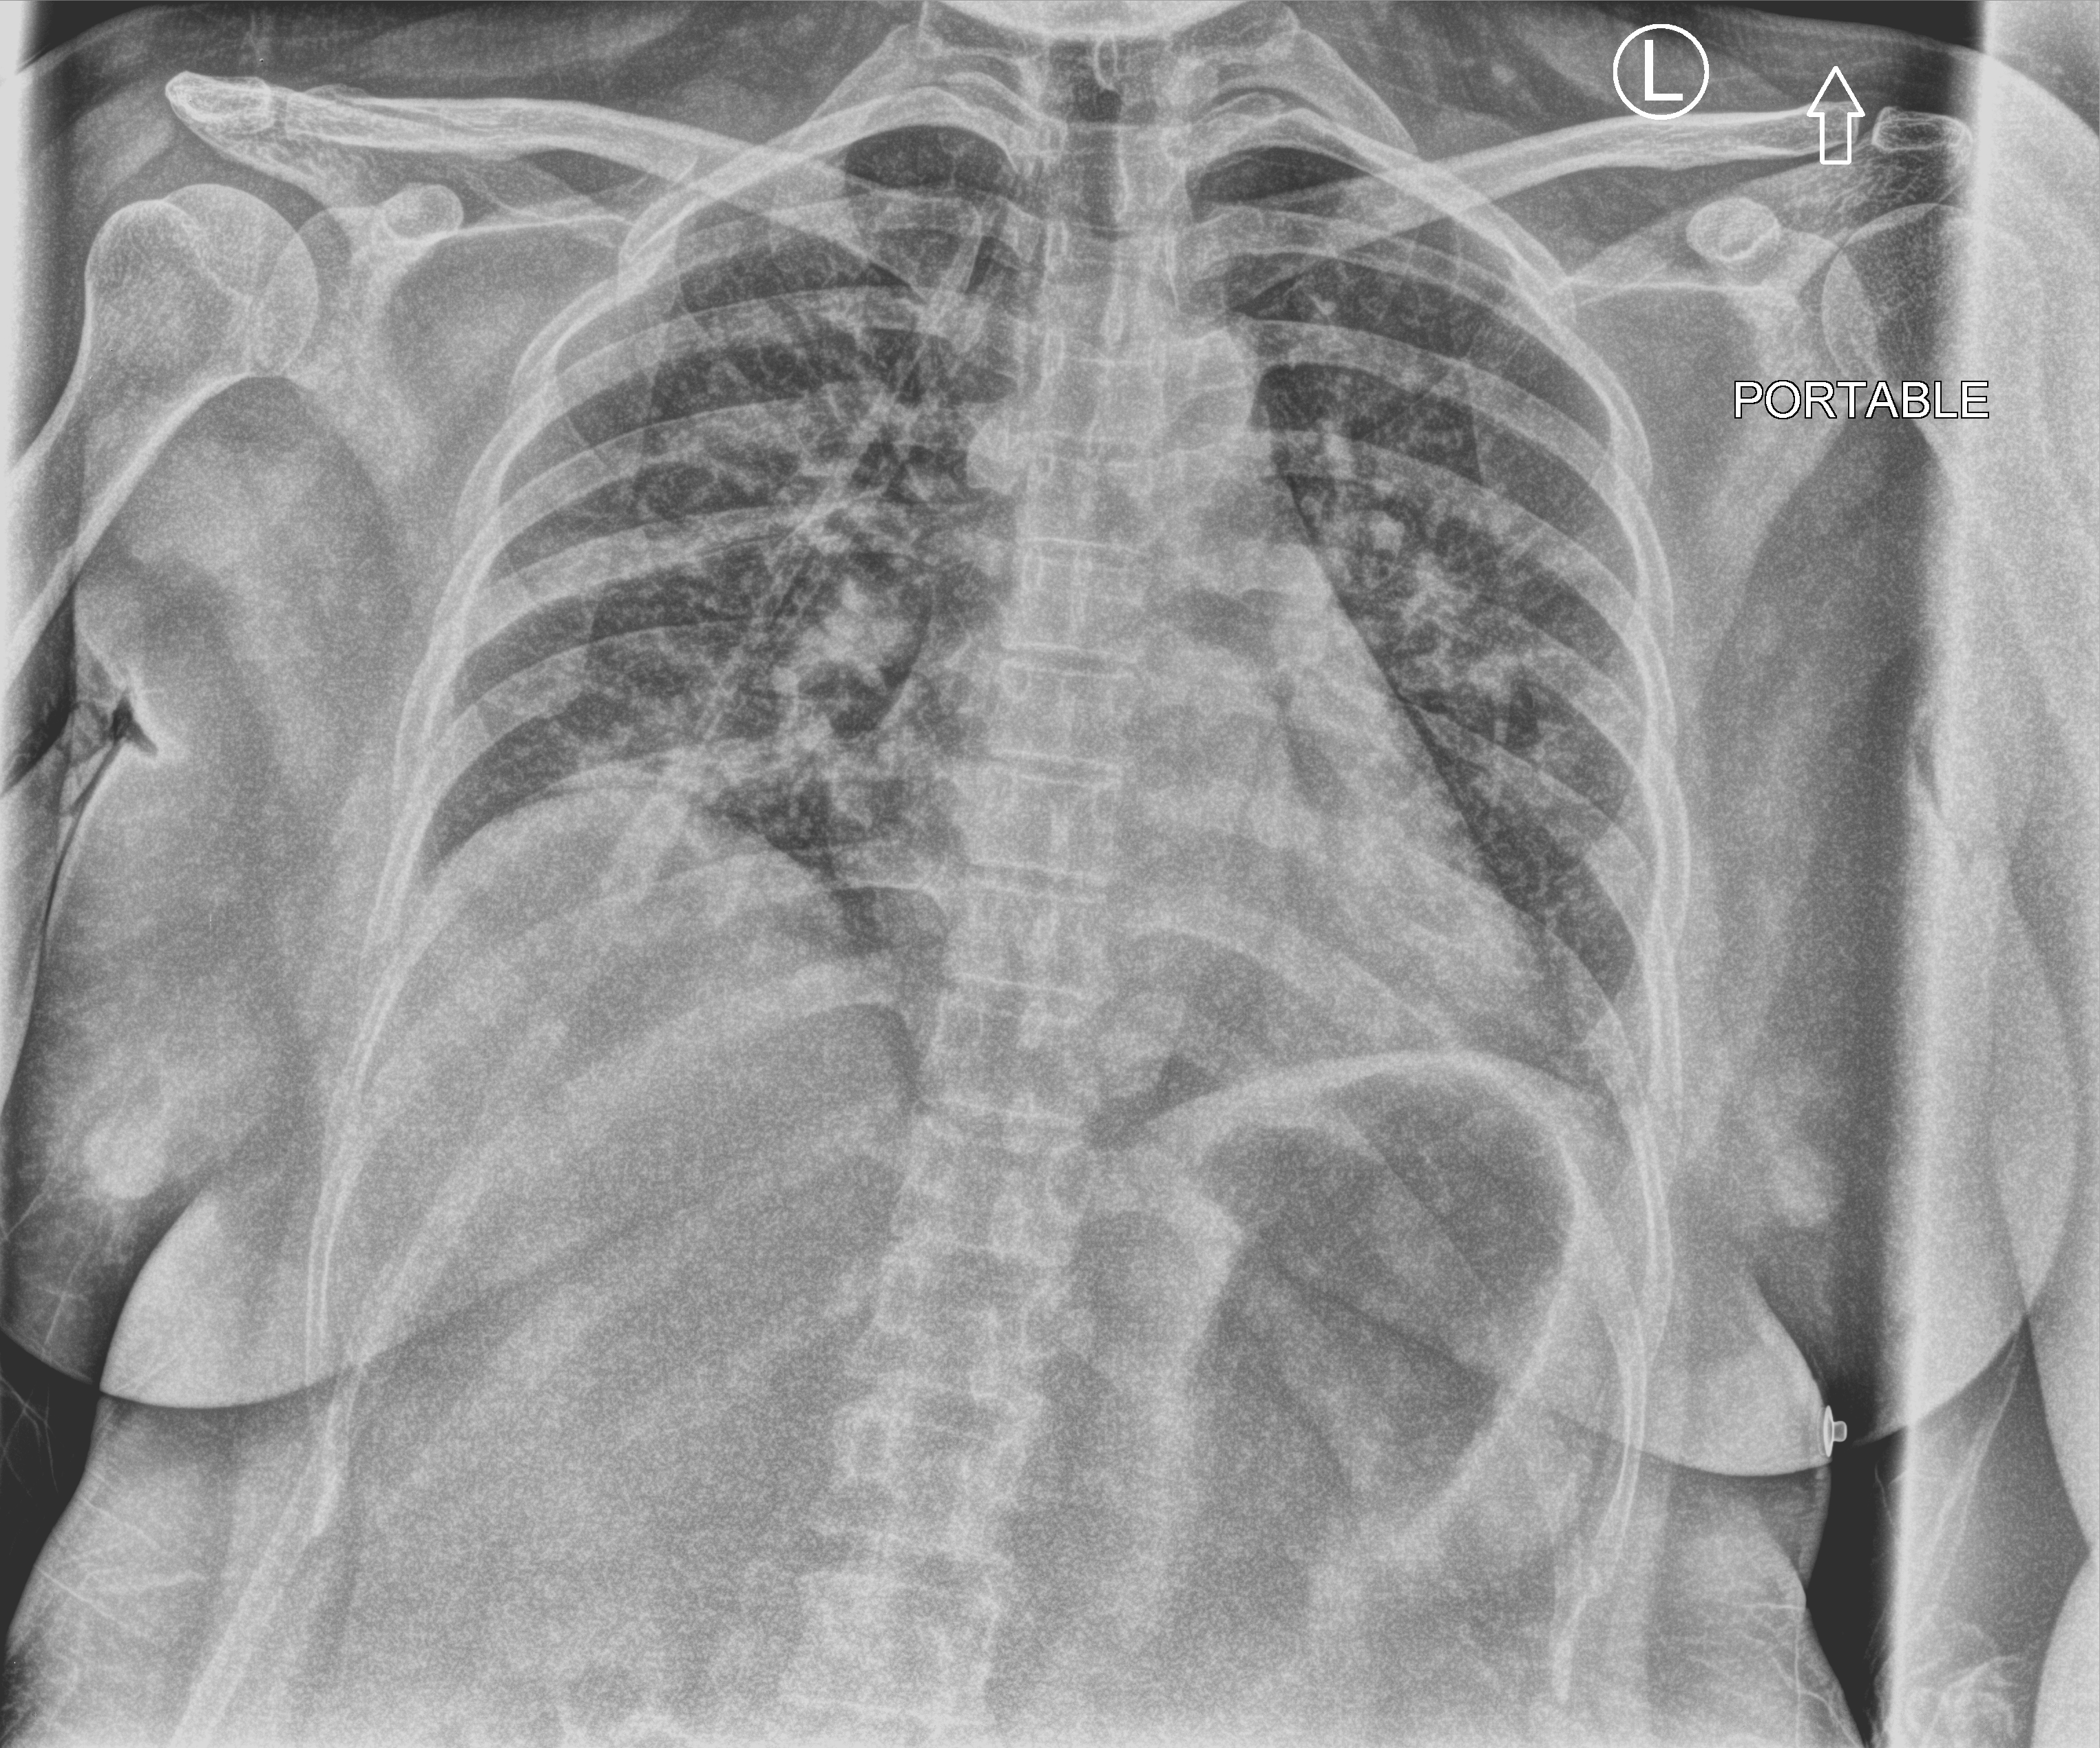
Bedside chest radiograph (computed radiography). Female patient hospitalised with COVID-19, age 18–59 years.
Admission-level facts for this patient (not findings on this image; timing relative to this image not recorded):
- mechanically ventilated during this hospital stay: no
- admitted to intensive care during this hospital stay: no